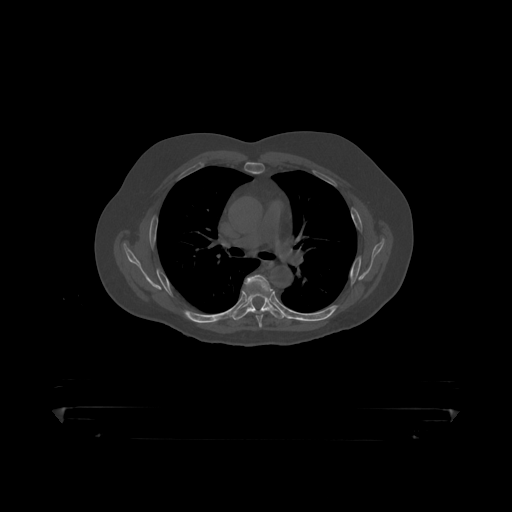
CT including the spine, one axial slice; position 309 of 390 along the scan axis; reconstruction kernel STANDARD; bone window (W 1800 / L 400 HU); 512 × 512 image matrix. Patient: male, 60 years. From the clinical record (not read from this slice): primary cancer: prostate.
Annotated regions visible in this slice (semi-automatically segmented with operator editing):
- T5 vertebra: bounding box [x1, y1, x2, y2] px = [245, 275, 272, 319]
- T6 vertebra: [235, 291, 282, 318]